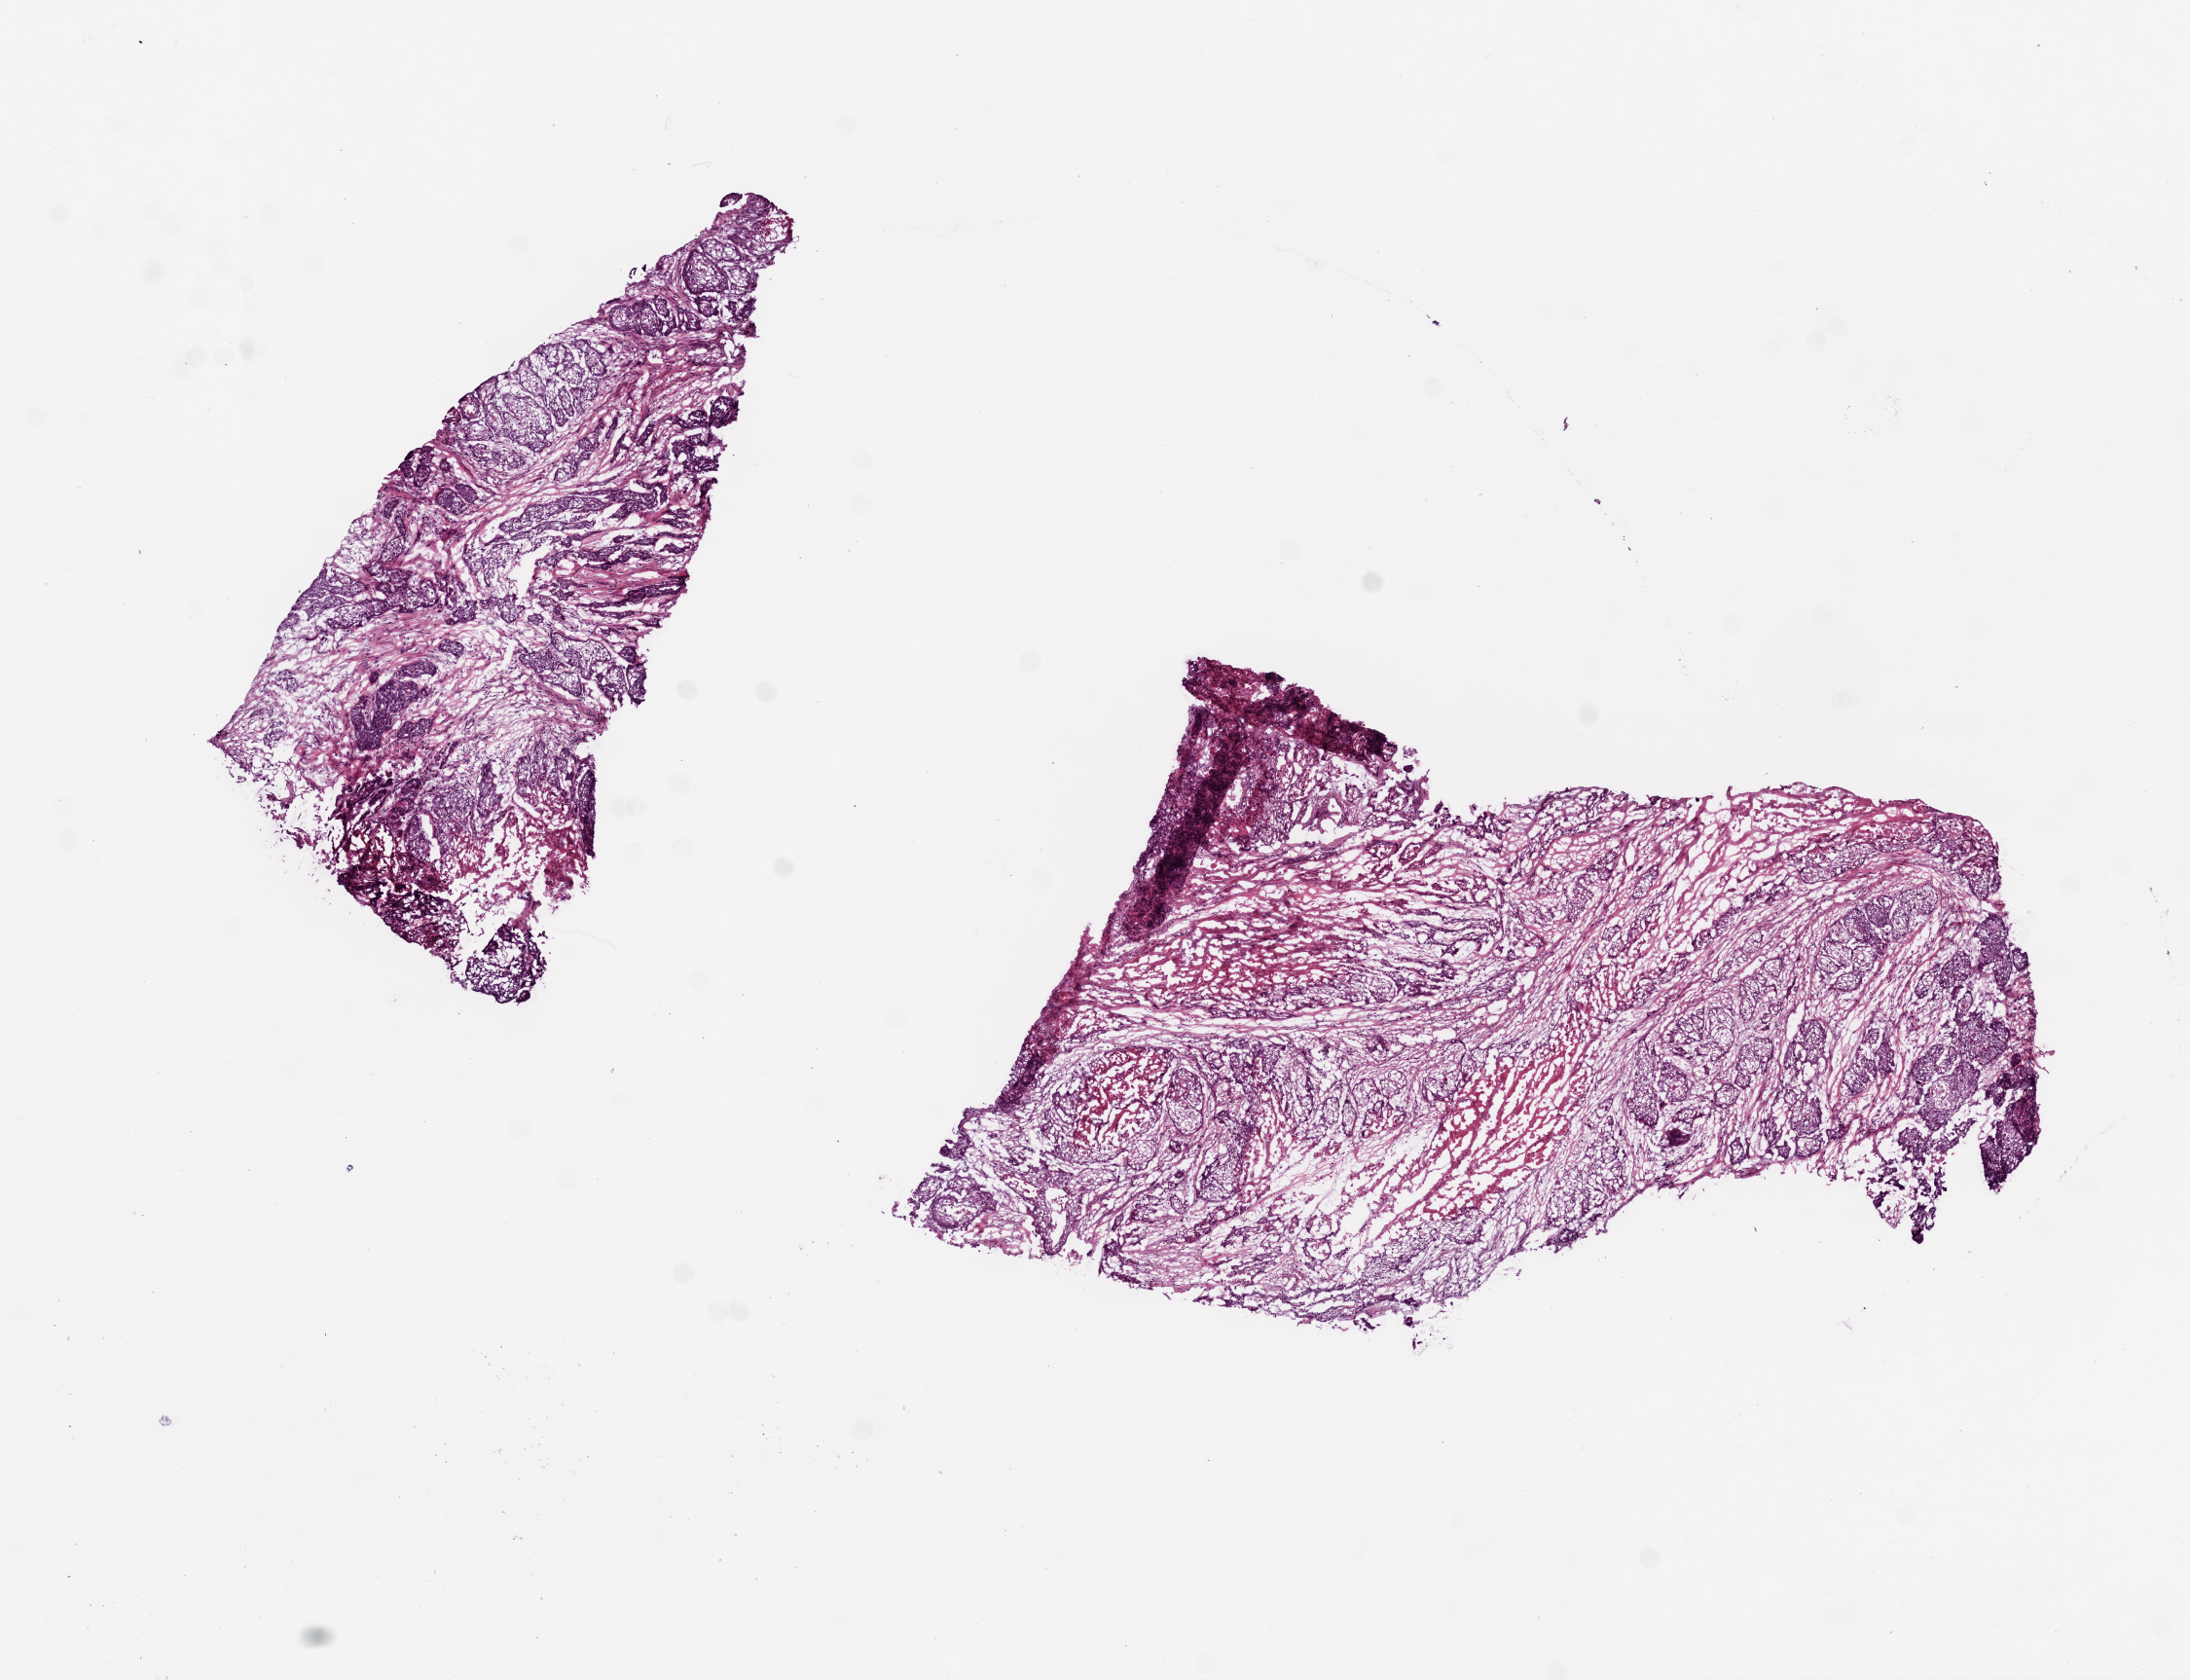
Whole-slide histology image, H&E-stained, whole scanned area (about 9.0 x 6.9 mm, from a 20x scan) shown as a low-resolution overview. Frozen section. Head and neck, primary tumour sample. Patient: female, age at initial diagnosis 63 years. Histologic grade: G3 (poorly differentiated). Slide review estimates, as recorded: tumour cells 55%, tumour nuclei 80%, normal cells 0%, stromal cells 40%, necrosis 5%.
AJCC pathologic stage: IVA (7th edition). Pathologic diagnosis: Squamous cell carcinoma, NOS (overlapping lesion of lip, oral cavity and pharynx). Lymph nodes positive (case pathology): 3 of 52 examined.